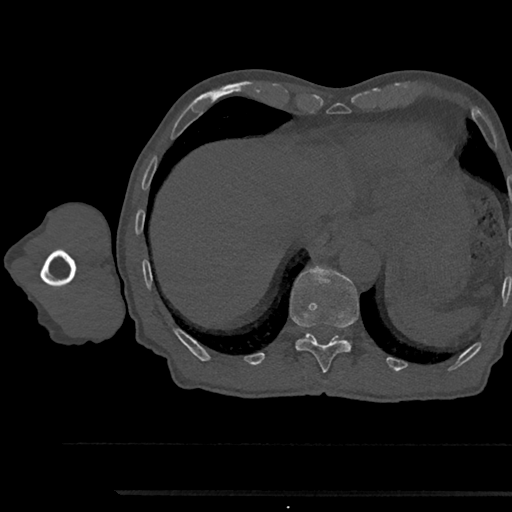
CT including the spine, one axial slice. Slice 776 of 797 in the series (ordered by position). Reconstruction kernel Br40s/3. 120 kVp. Bone window (W 1800 / L 400 HU). 0.5 mm slice thickness. 512 × 512 image matrix. Patient: male, 79 years. Case-level facts recorded for this patient, not image findings: primary cancer: prostate.
Annotated regions visible in this slice (semi-automatically segmented with operator editing):
- T11 vertebra: bounding box [x1, y1, x2, y2] px = [290, 266, 359, 374]